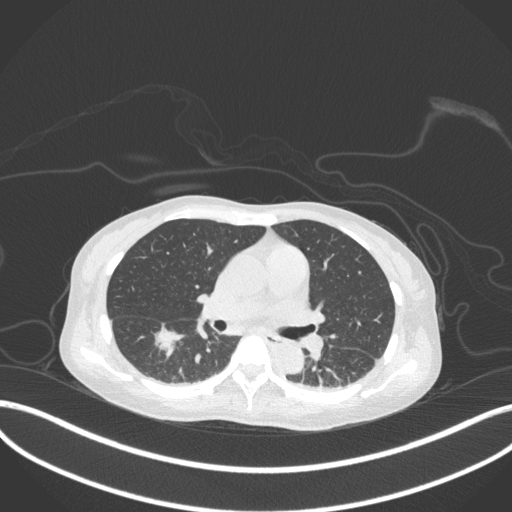
Chest CT, one axial slice. Position 172 of 260 along the scan axis. Reconstruction kernel B31f. 120 kVp. Lung window (W 1500 / L -600 HU). 512 × 512 image matrix. Female patient, age 44 years. Case-level facts recorded for this patient, not image findings: clinical TNM (as recorded): T1c N0 M0.
Structures marked on this image (rectangle marked by the reading radiologist):
- lung tumour (recorded histology: adenocarcinoma): bounding box [x1, y1, x2, y2] px = [146, 321, 187, 359]